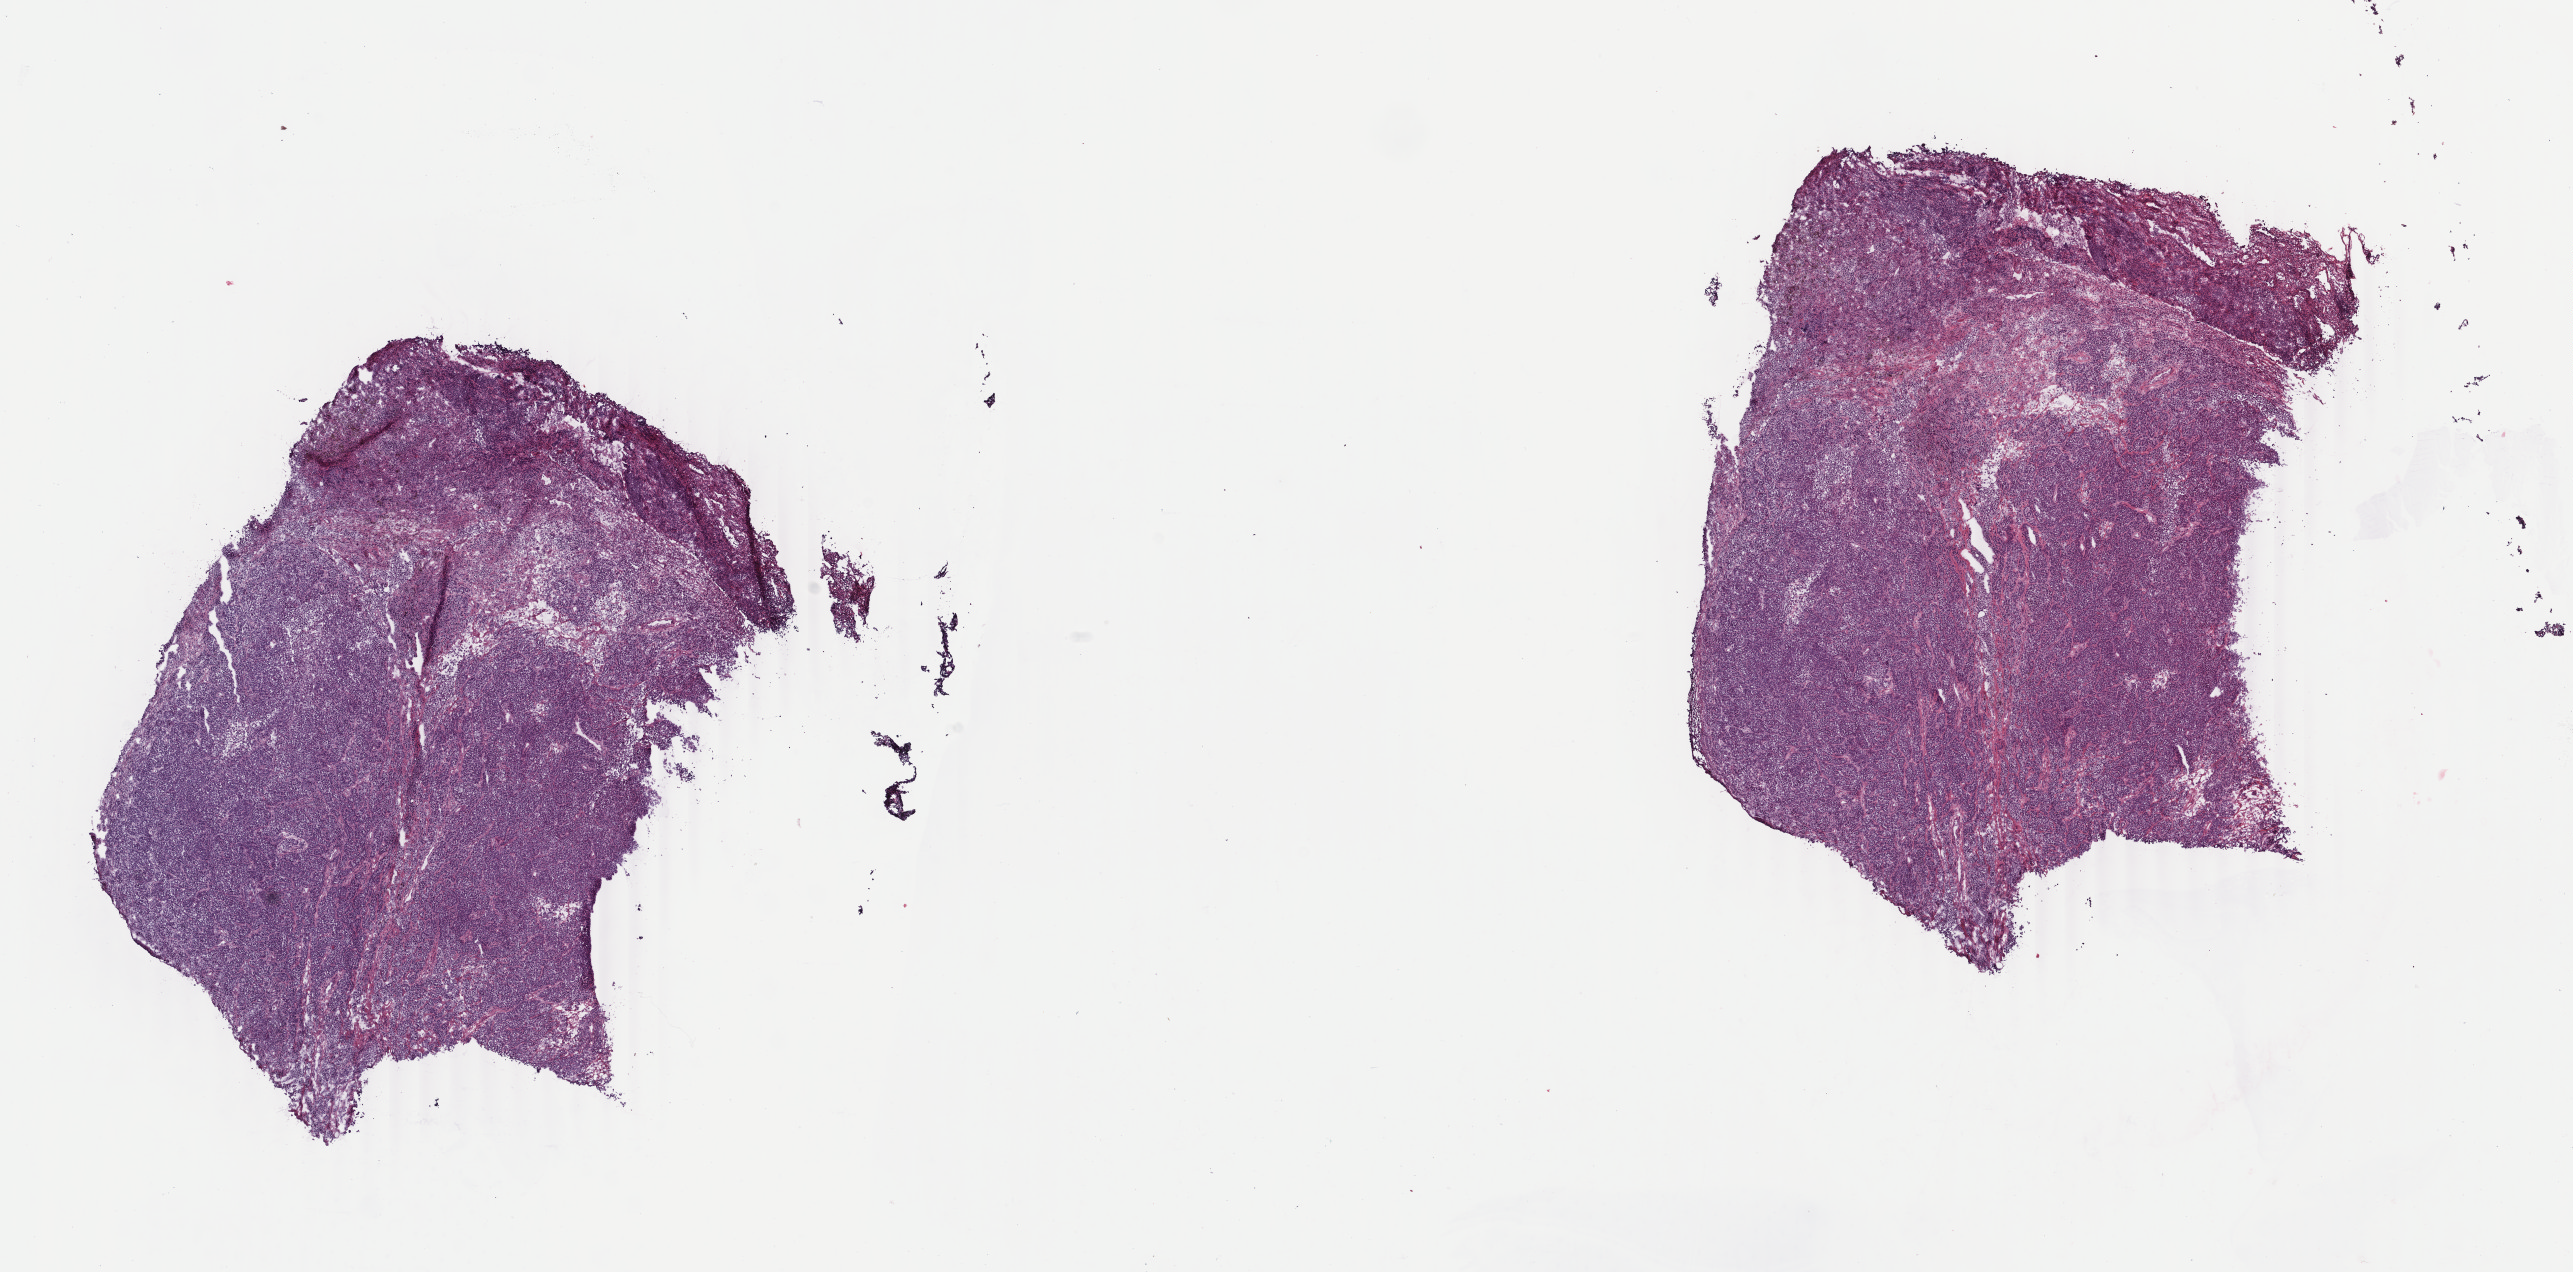
Whole-slide histology image, H&E-stained, whole scanned area (about 20.5 x 10.1 mm) shown as a low-resolution overview. Frozen section. Metastatic tumour sample, sampled site: lymph node. Male patient; age at initial diagnosis 52 years.
This section: metastatic tumour tissue. Patient diagnosis: Malignant melanoma, NOS.